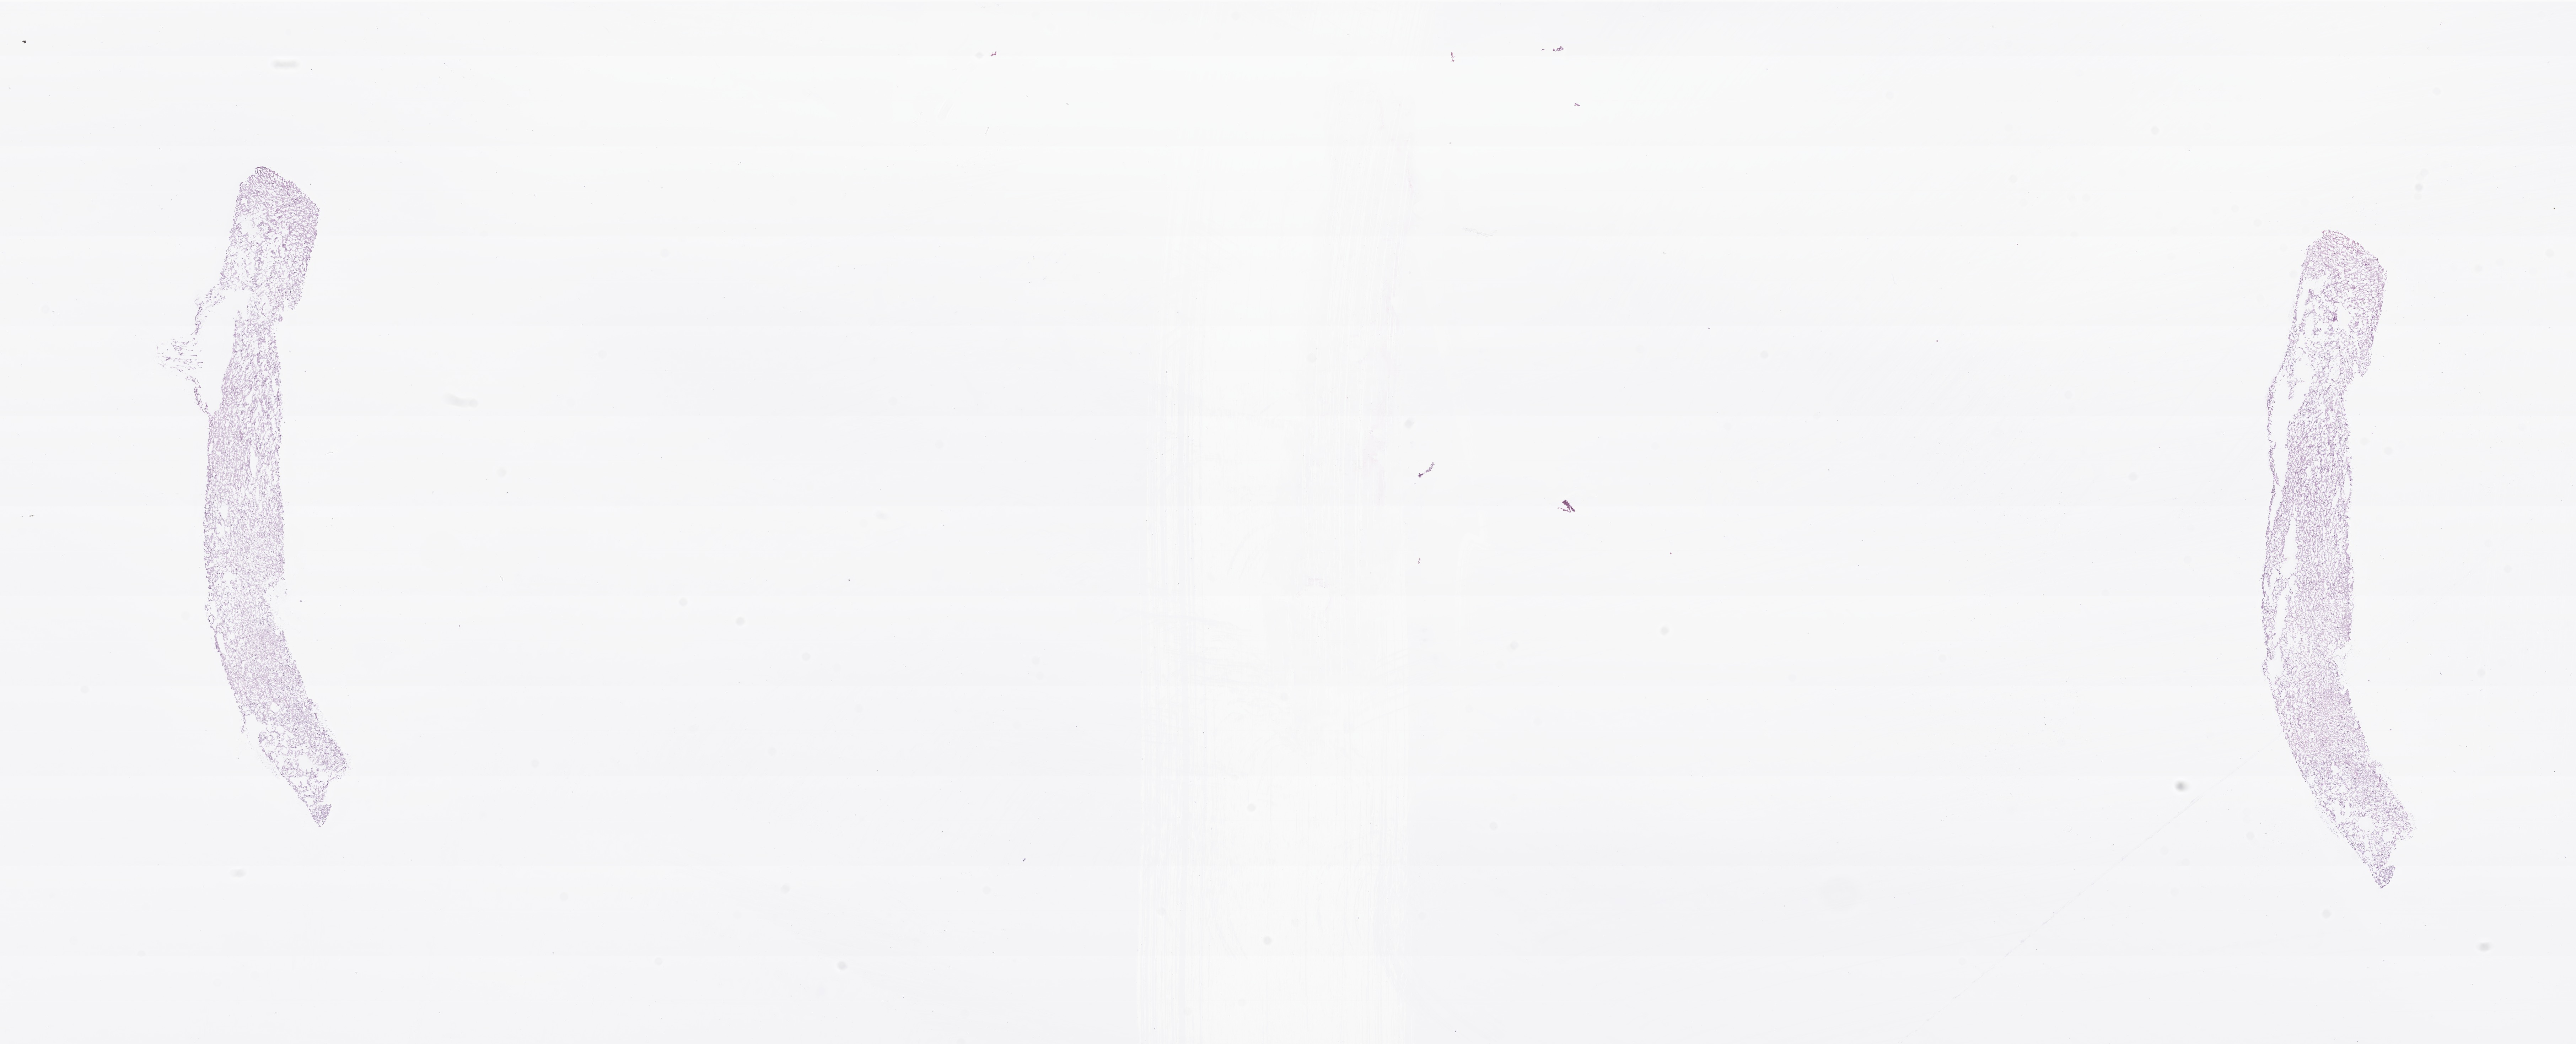
Haematoxylin and eosin whole-slide image of tumor tissue from the brain — whole scanned area (about 30.5 x 12.4 mm) shown as a low-resolution overview. Frozen section. Patient: female, age 116 months (9 years 8 months).
Recorded diagnosis: Oligoastrocytoma, NOS.